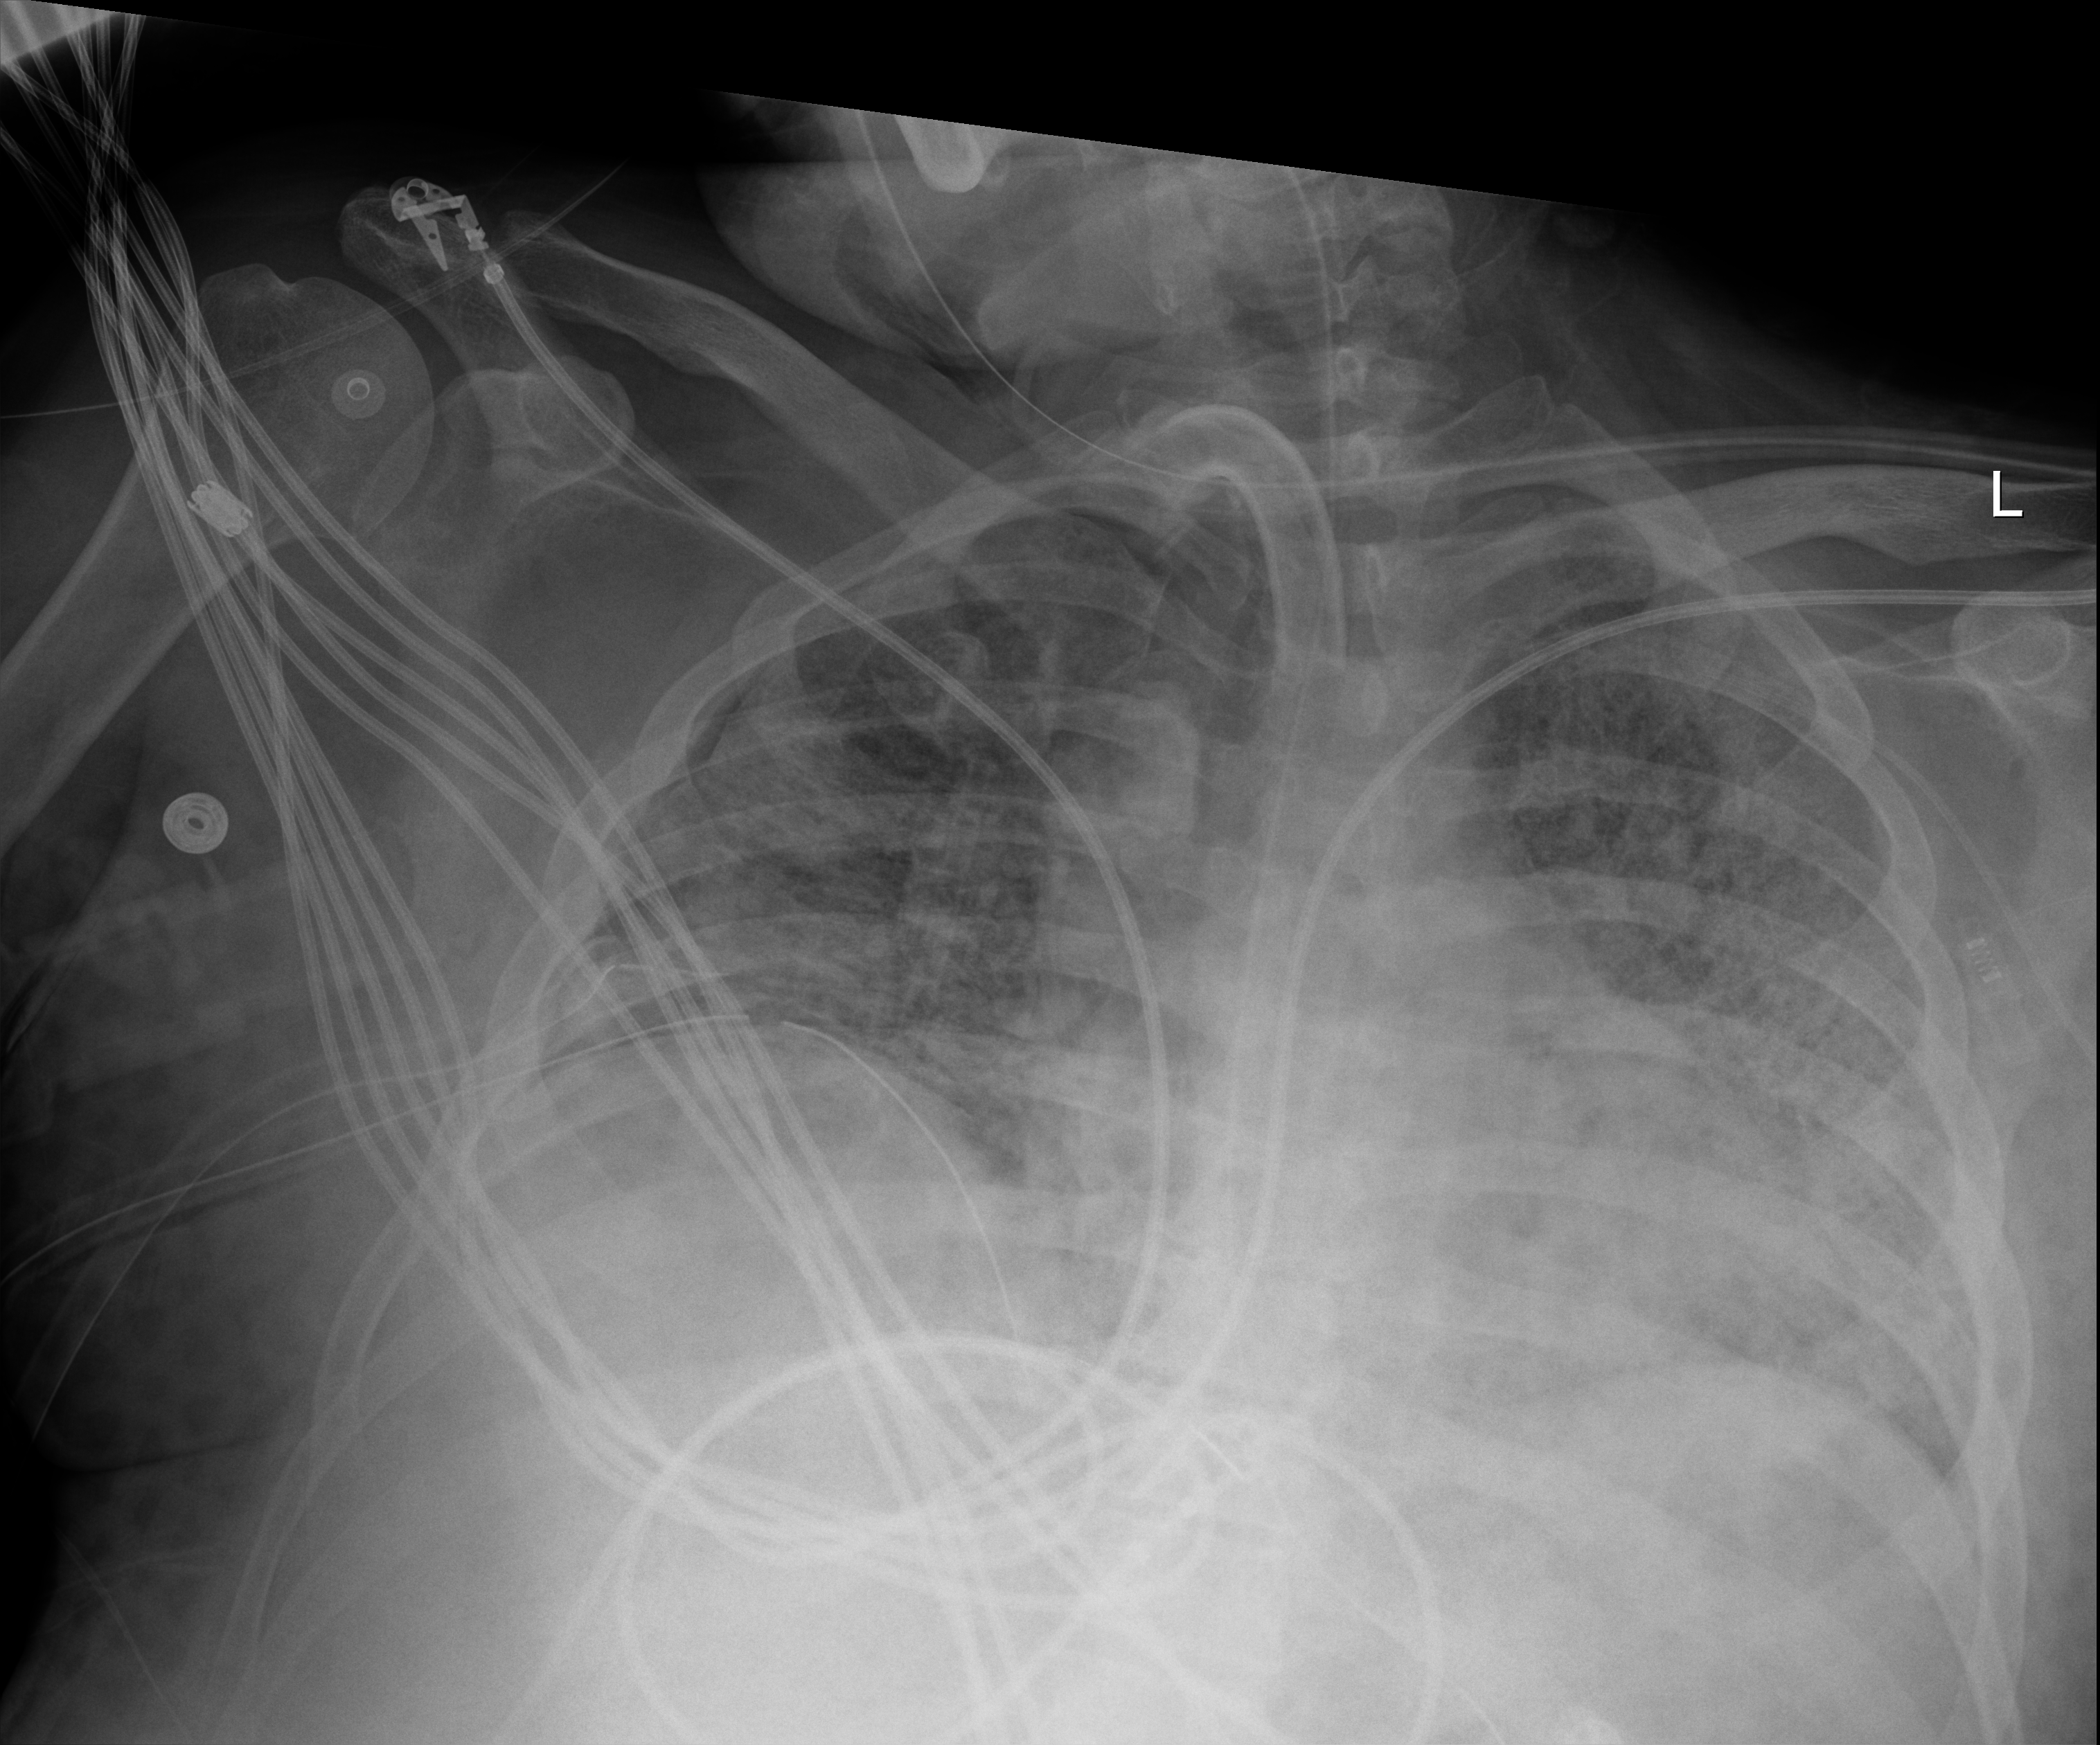
Chest X-ray. Patient hospitalised with COVID-19; male, aged 18–59 years.
Admission-level facts for this patient (not findings on this image; timing relative to this image not recorded): length of hospital stay: 80 days; chronic kidney disease (admission record): no; mechanically ventilated during this hospital stay: yes.